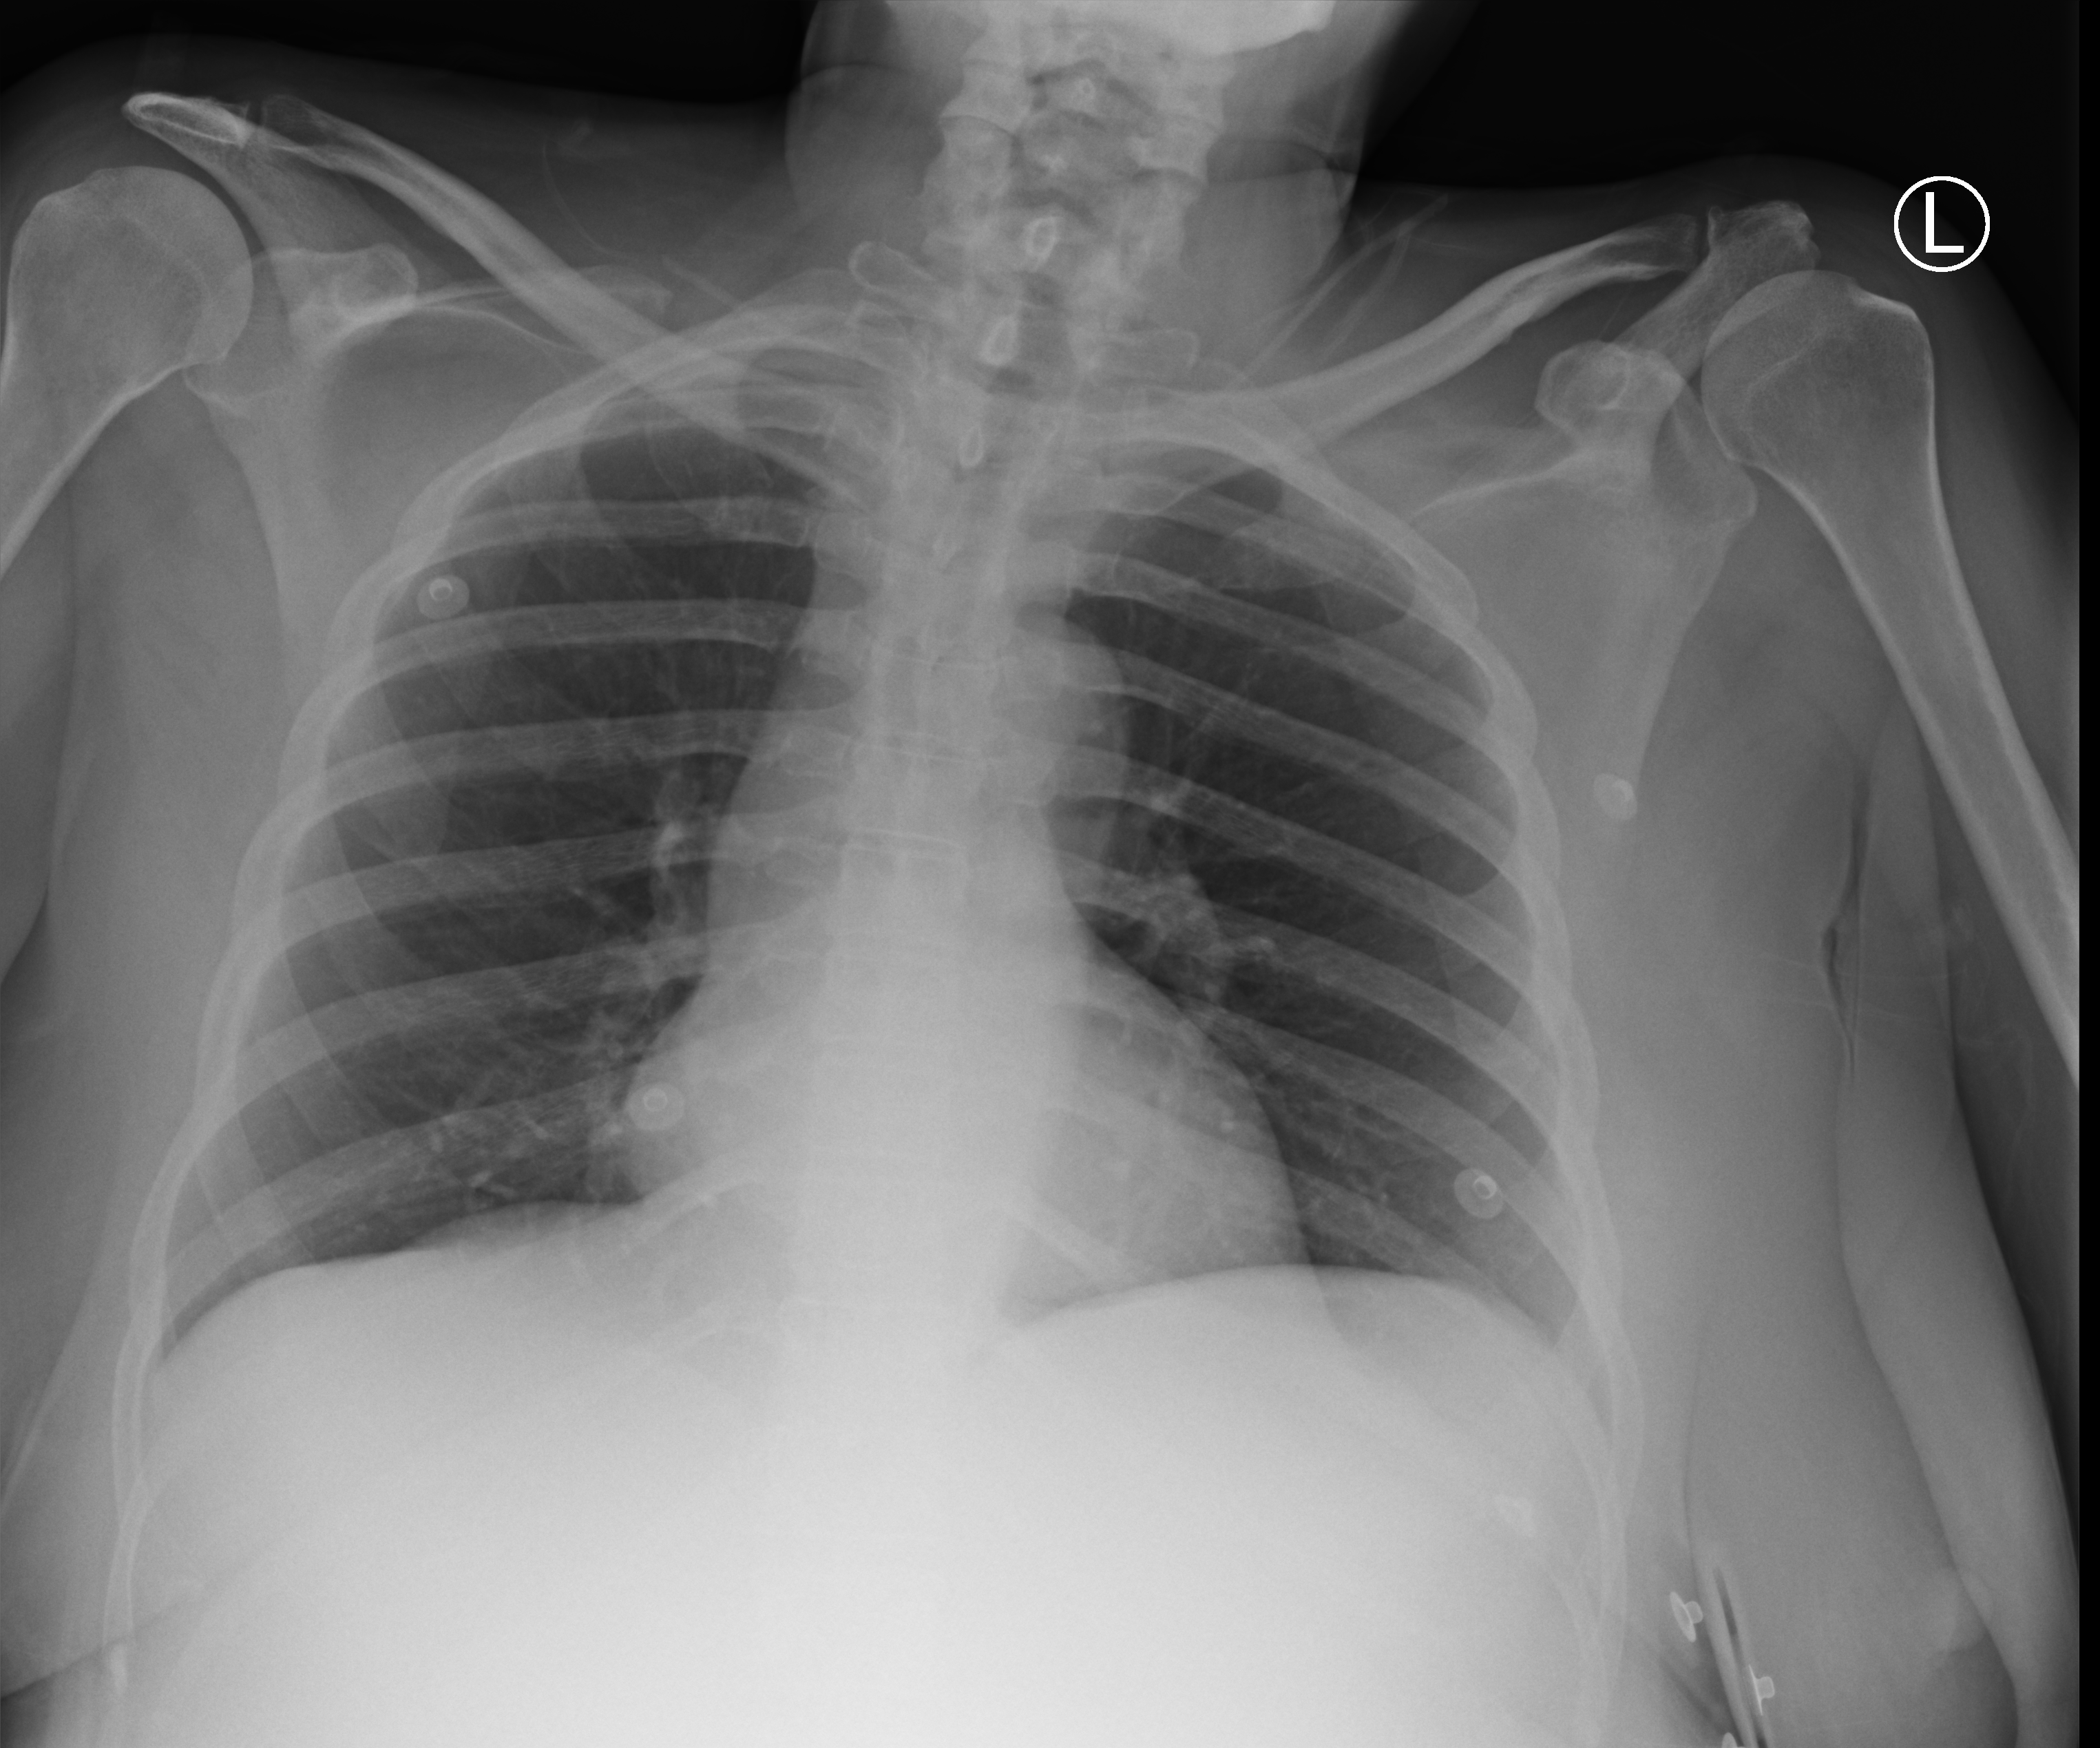
Bedside chest radiograph (computed radiography), anteroposterior (AP) projection. Female patient hospitalised with COVID-19, age 18–59 years.
Hospital-stay facts (about this admission, not read from this image; timing relative to this image not recorded): mechanically ventilated during this hospital stay: no.